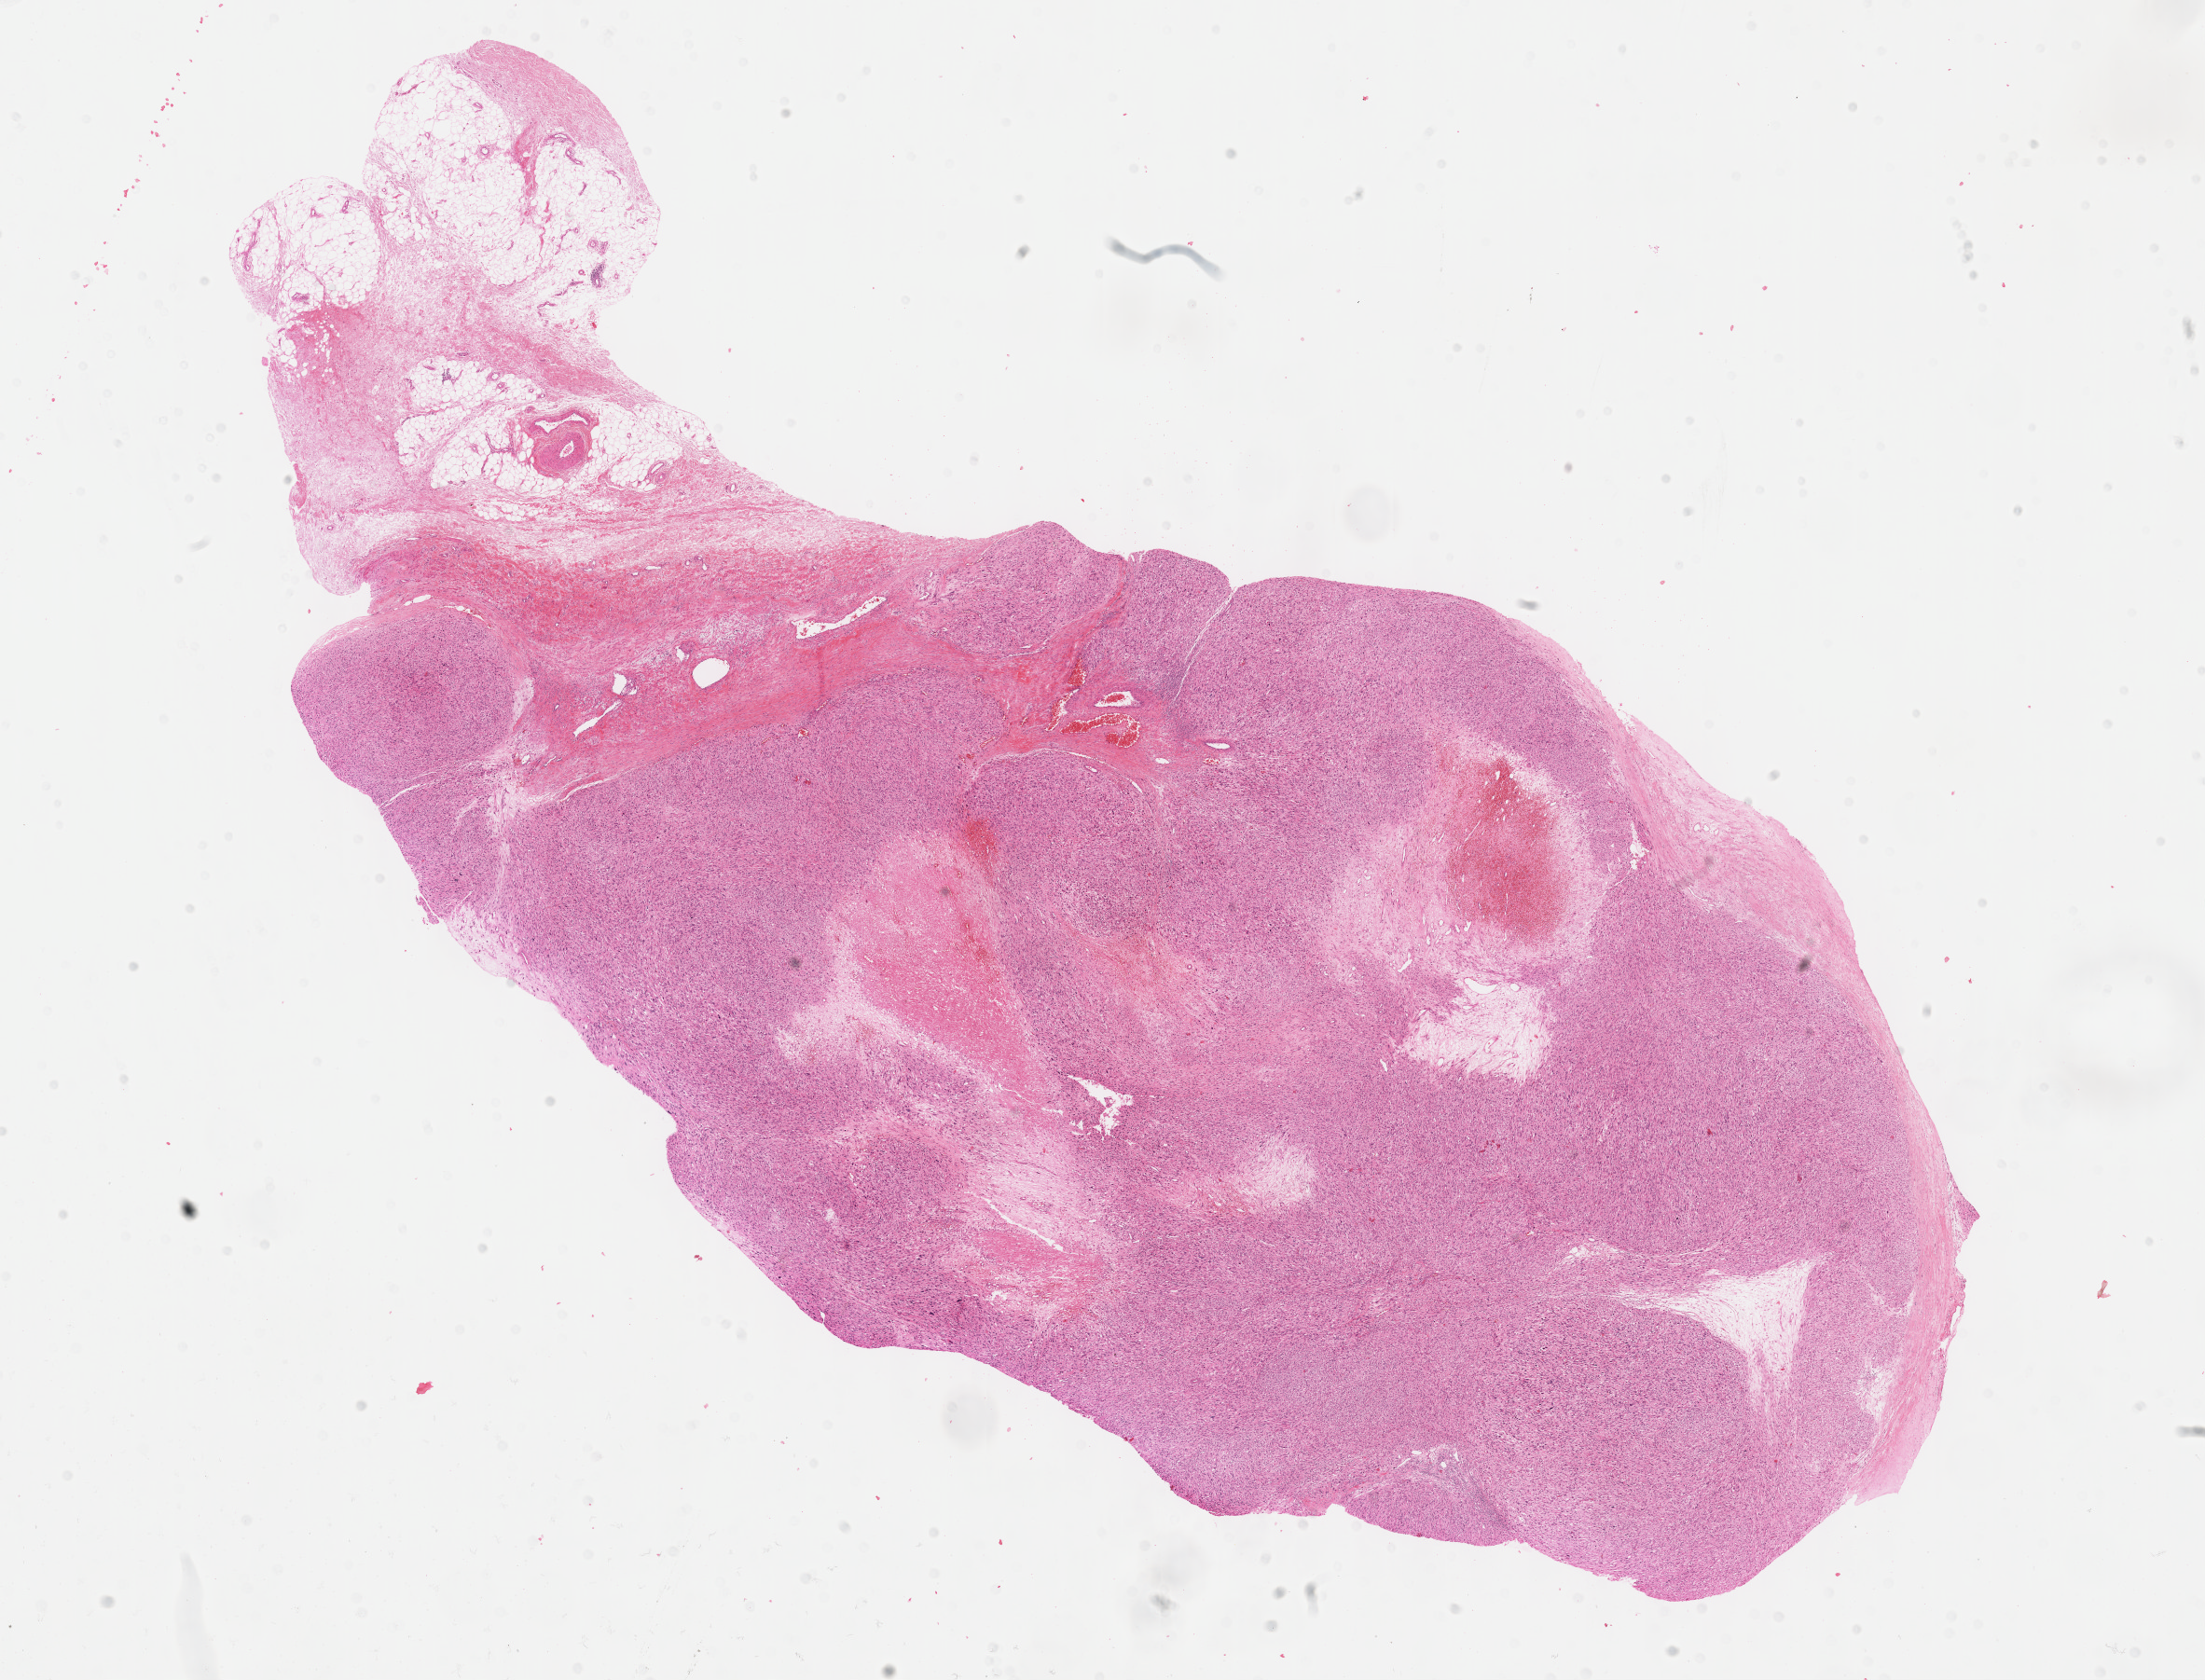
H&E-stained whole-slide image — whole scanned area (about 19.1 x 14.6 mm, acquisition: 40x scan) shown as a low-resolution overview. Formalin-fixed paraffin-embedded (FFPE) diagnostic section. Primary tumour sample from the bones, joints and articular cartilage of limbs. Male, age 80 years at initial diagnosis.
Pathologic diagnosis: Leiomyosarcoma, NOS (long bones of lower limb and associated joints).